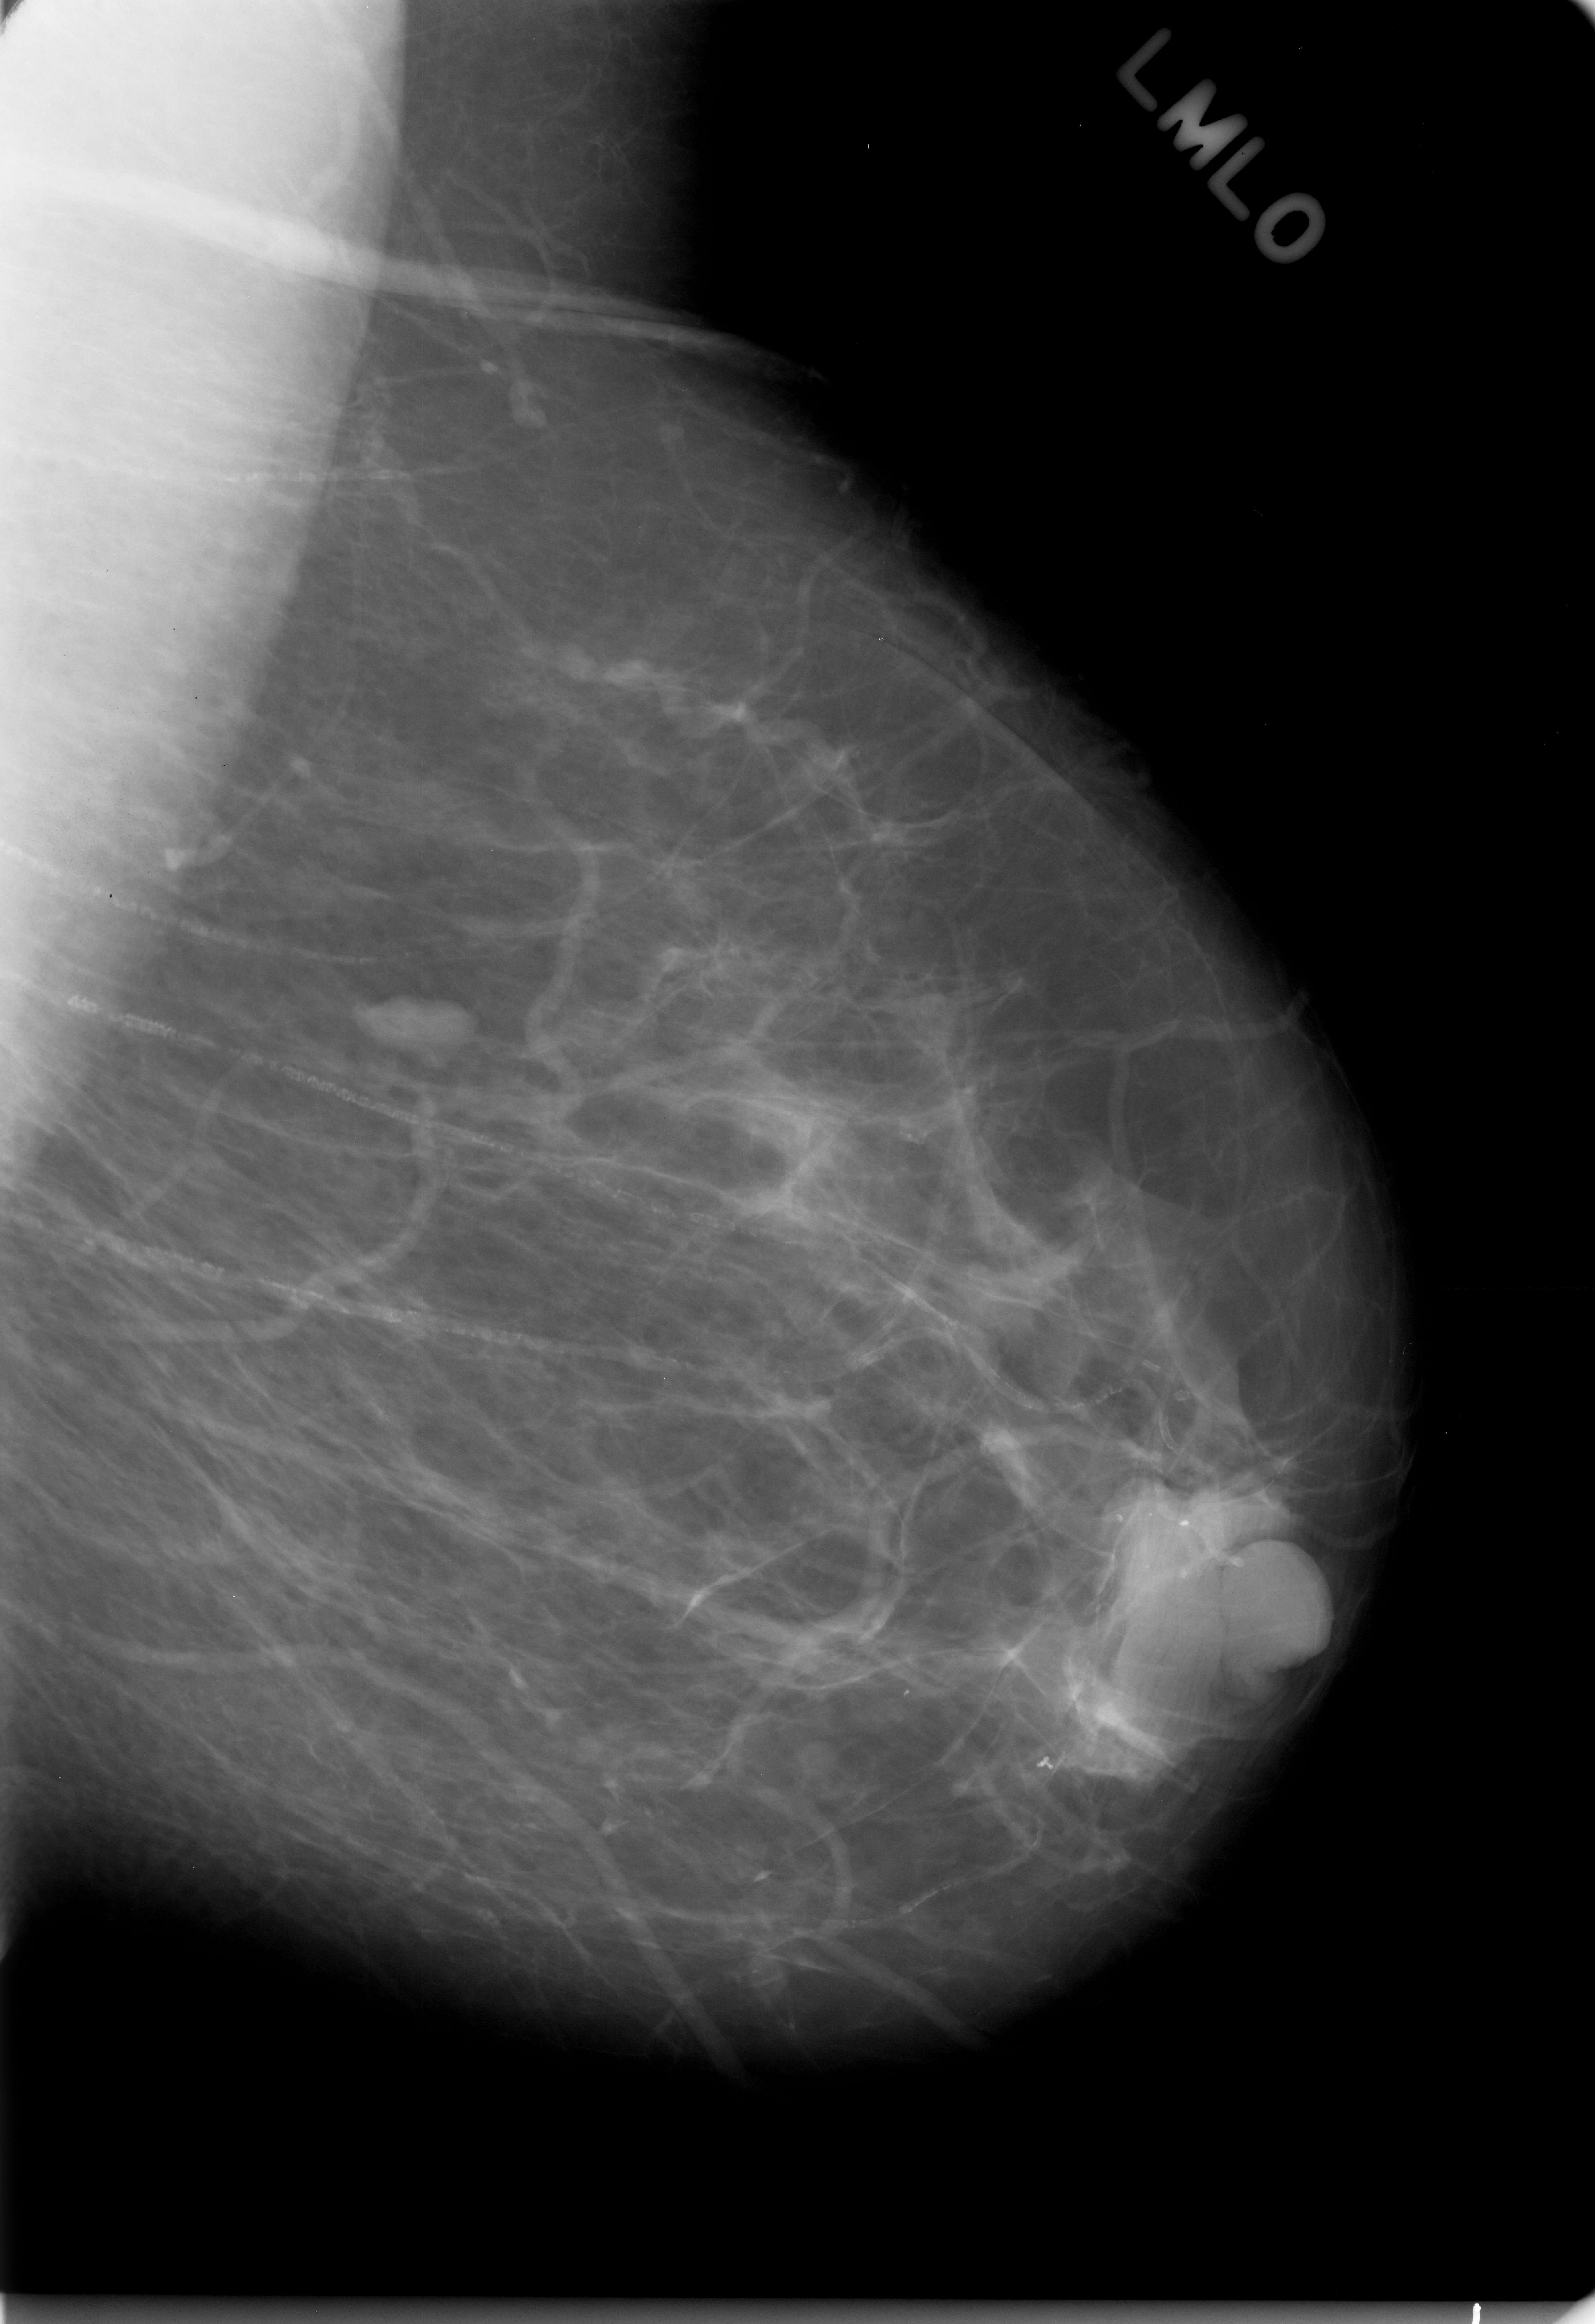
Scanned film-screen mammogram; left breast; mediolateral oblique (MLO) view; BI-RADS breast density category 1 (scale 1–4).
Abnormality record for this image: mass, shape oval, margins circumscribed; BI-RADS assessment category 2; pathology (as recorded): benign.